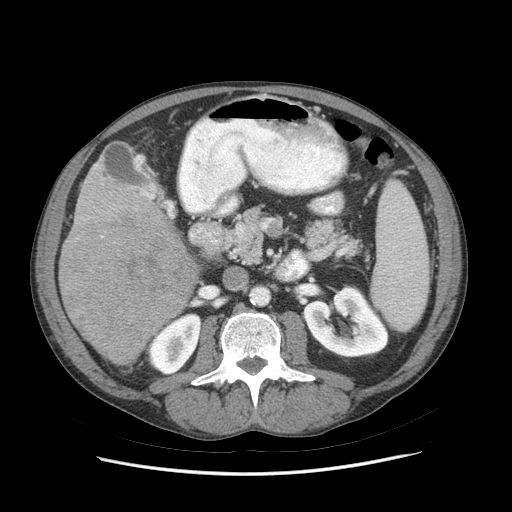
Contrast-enhanced abdominal CT (liver protocol), one axial slice; position 28 of 89 along the scan axis; soft-tissue window (W 400 / L 40 HU); 2.5 mm slice thickness; 512 × 512 image matrix, field of view 380 × 380 mm. Case-level facts recorded for this patient, not image findings: diagnosis: hepatocellular carcinoma (patient treated with transarterial chemoembolisation; whether this scan precedes or follows treatment is not stated here); TNM stage (as recorded): Stage-IIIB; Child-Pugh class: A.
Structures marked on this image (semi-automatically segmented with operator editing):
- liver parenchyma outside the tumour (the mass and vessels are separate outlines, so this box may not span the whole liver): bounding box <58,158,178,364> (left, top, right, bottom; pixels)
- mass: <60,204,197,363>